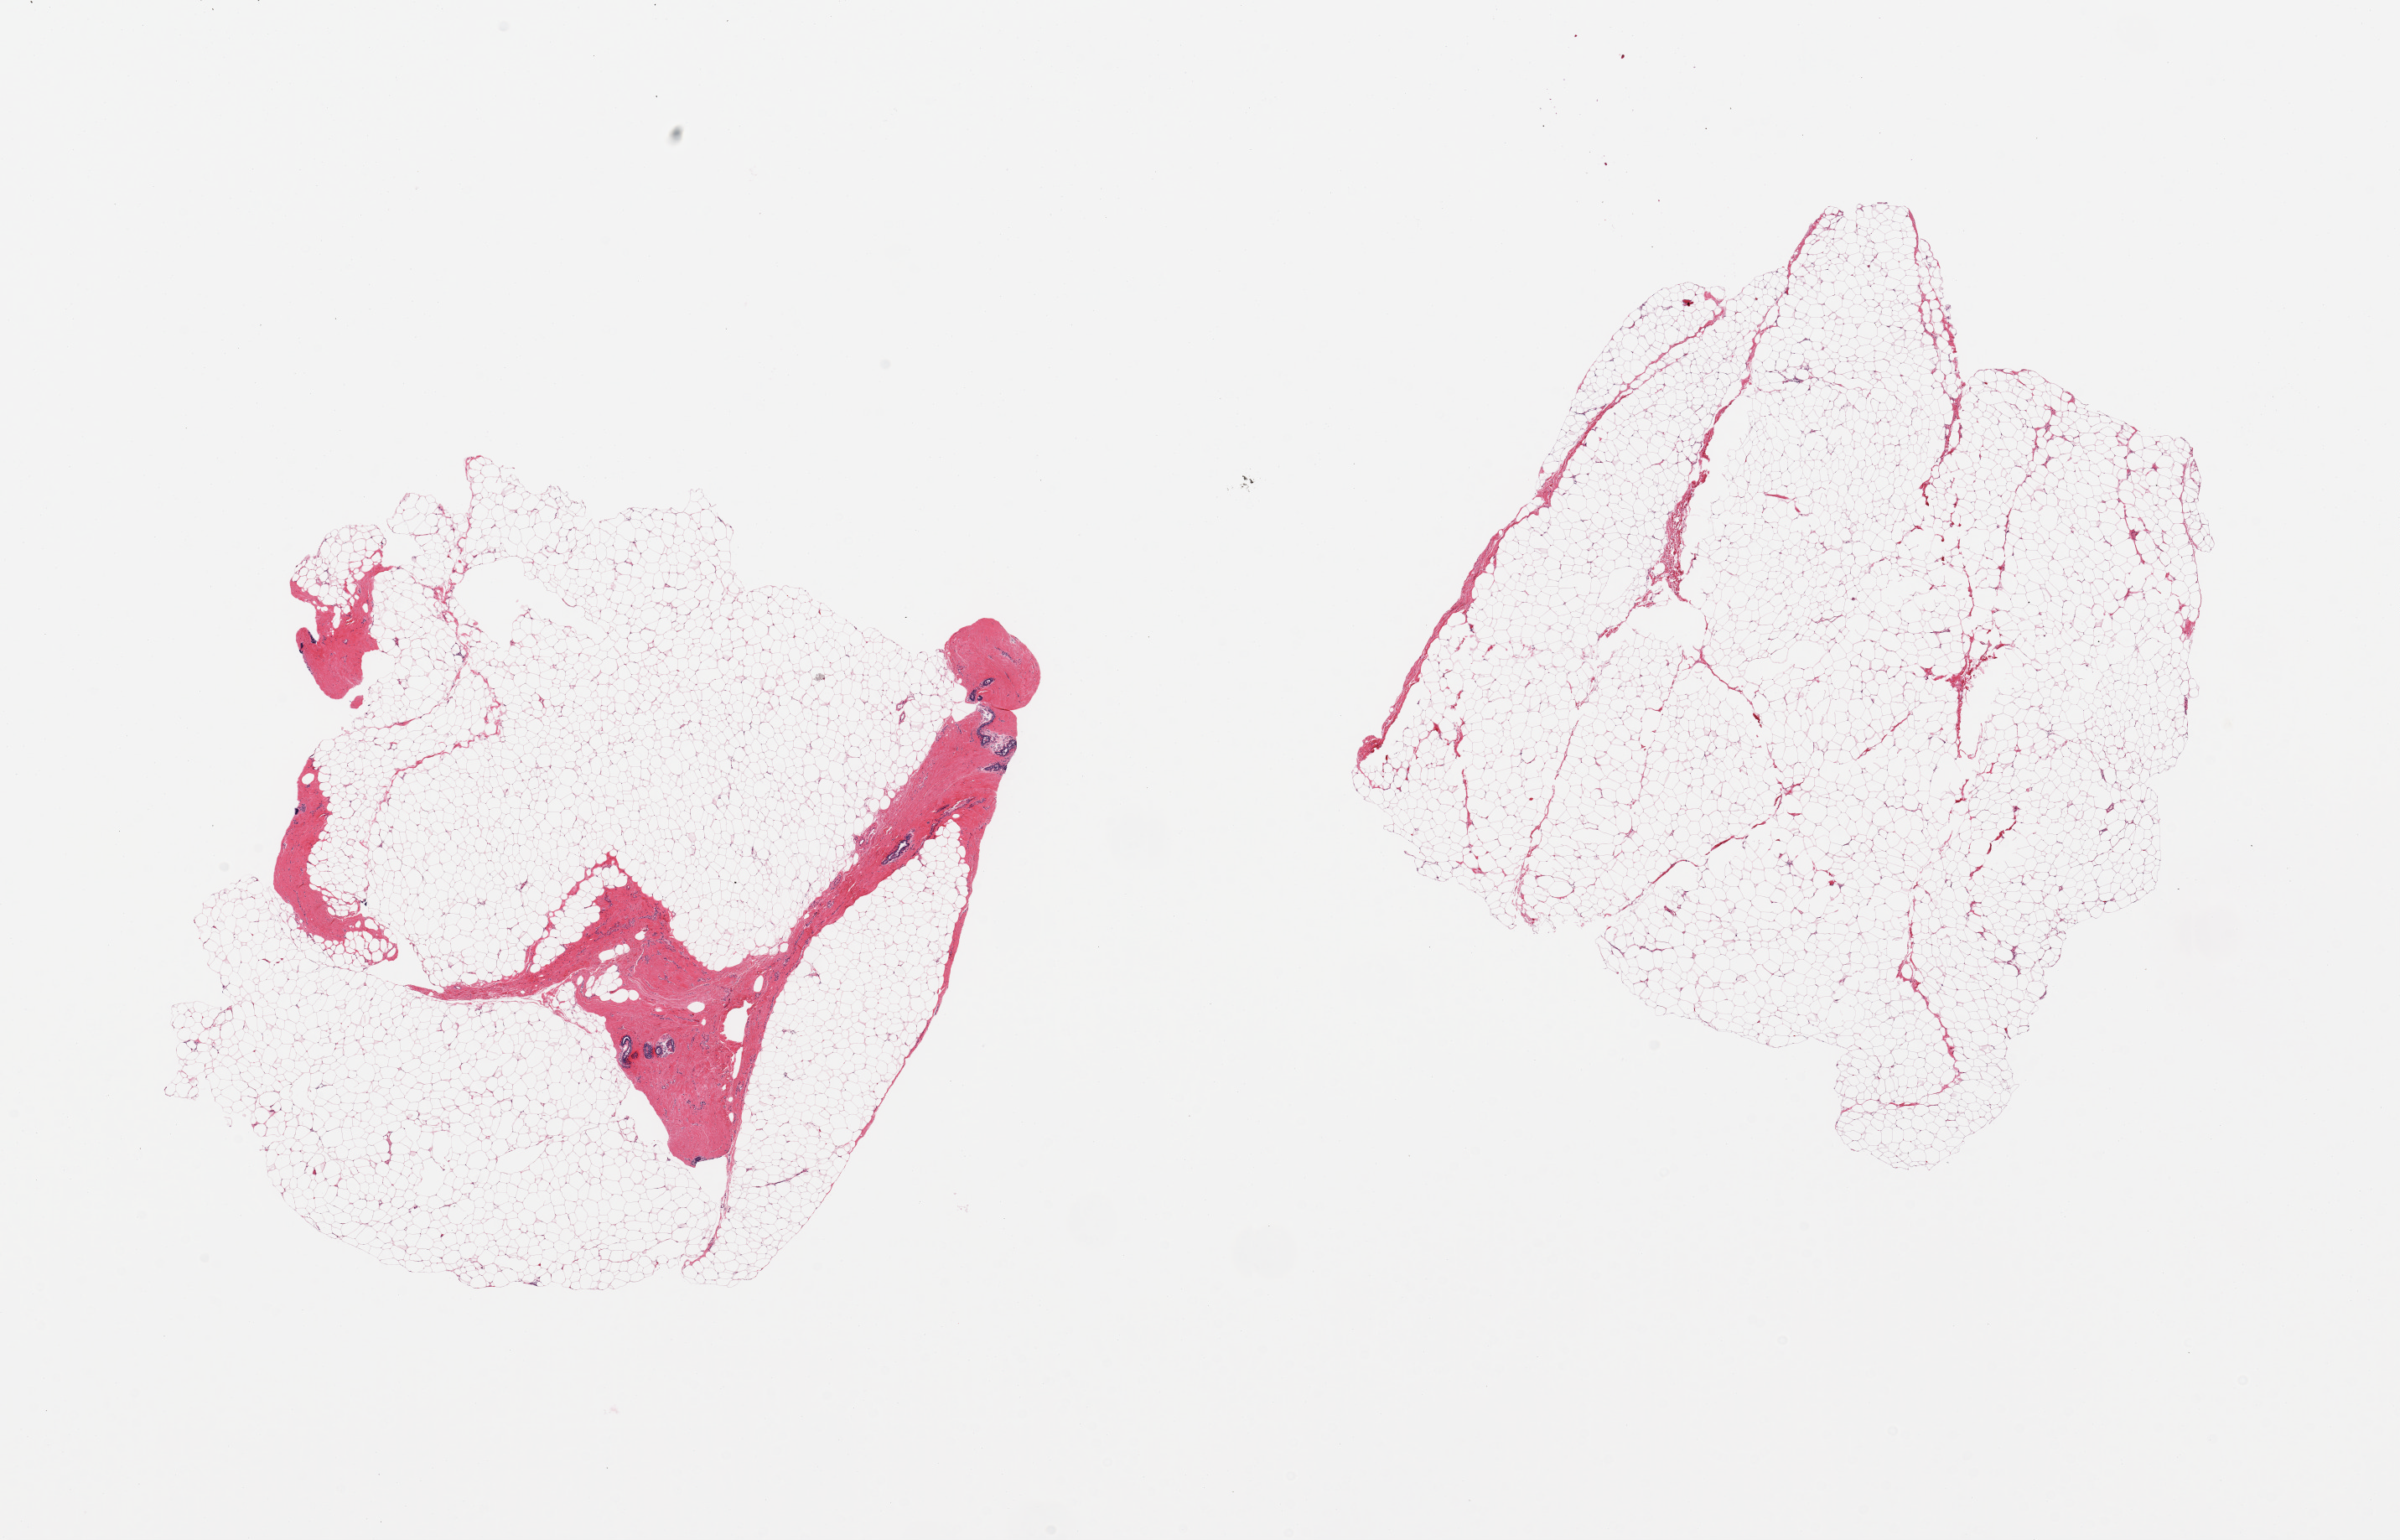
Whole-slide image, haematoxylin and eosin stain — whole scanned area (about 22.6 x 14.5 mm, from a 20x scan) shown as a low-resolution overview. PAXgene-fixed paraffin-embedded (PFPE) section. Section of breast (target tissue). Tissue donor sample. Donor: male.
Review note (as recorded): 2 pieces, focal gynecomastoid stromal and ductal hyperplasia.